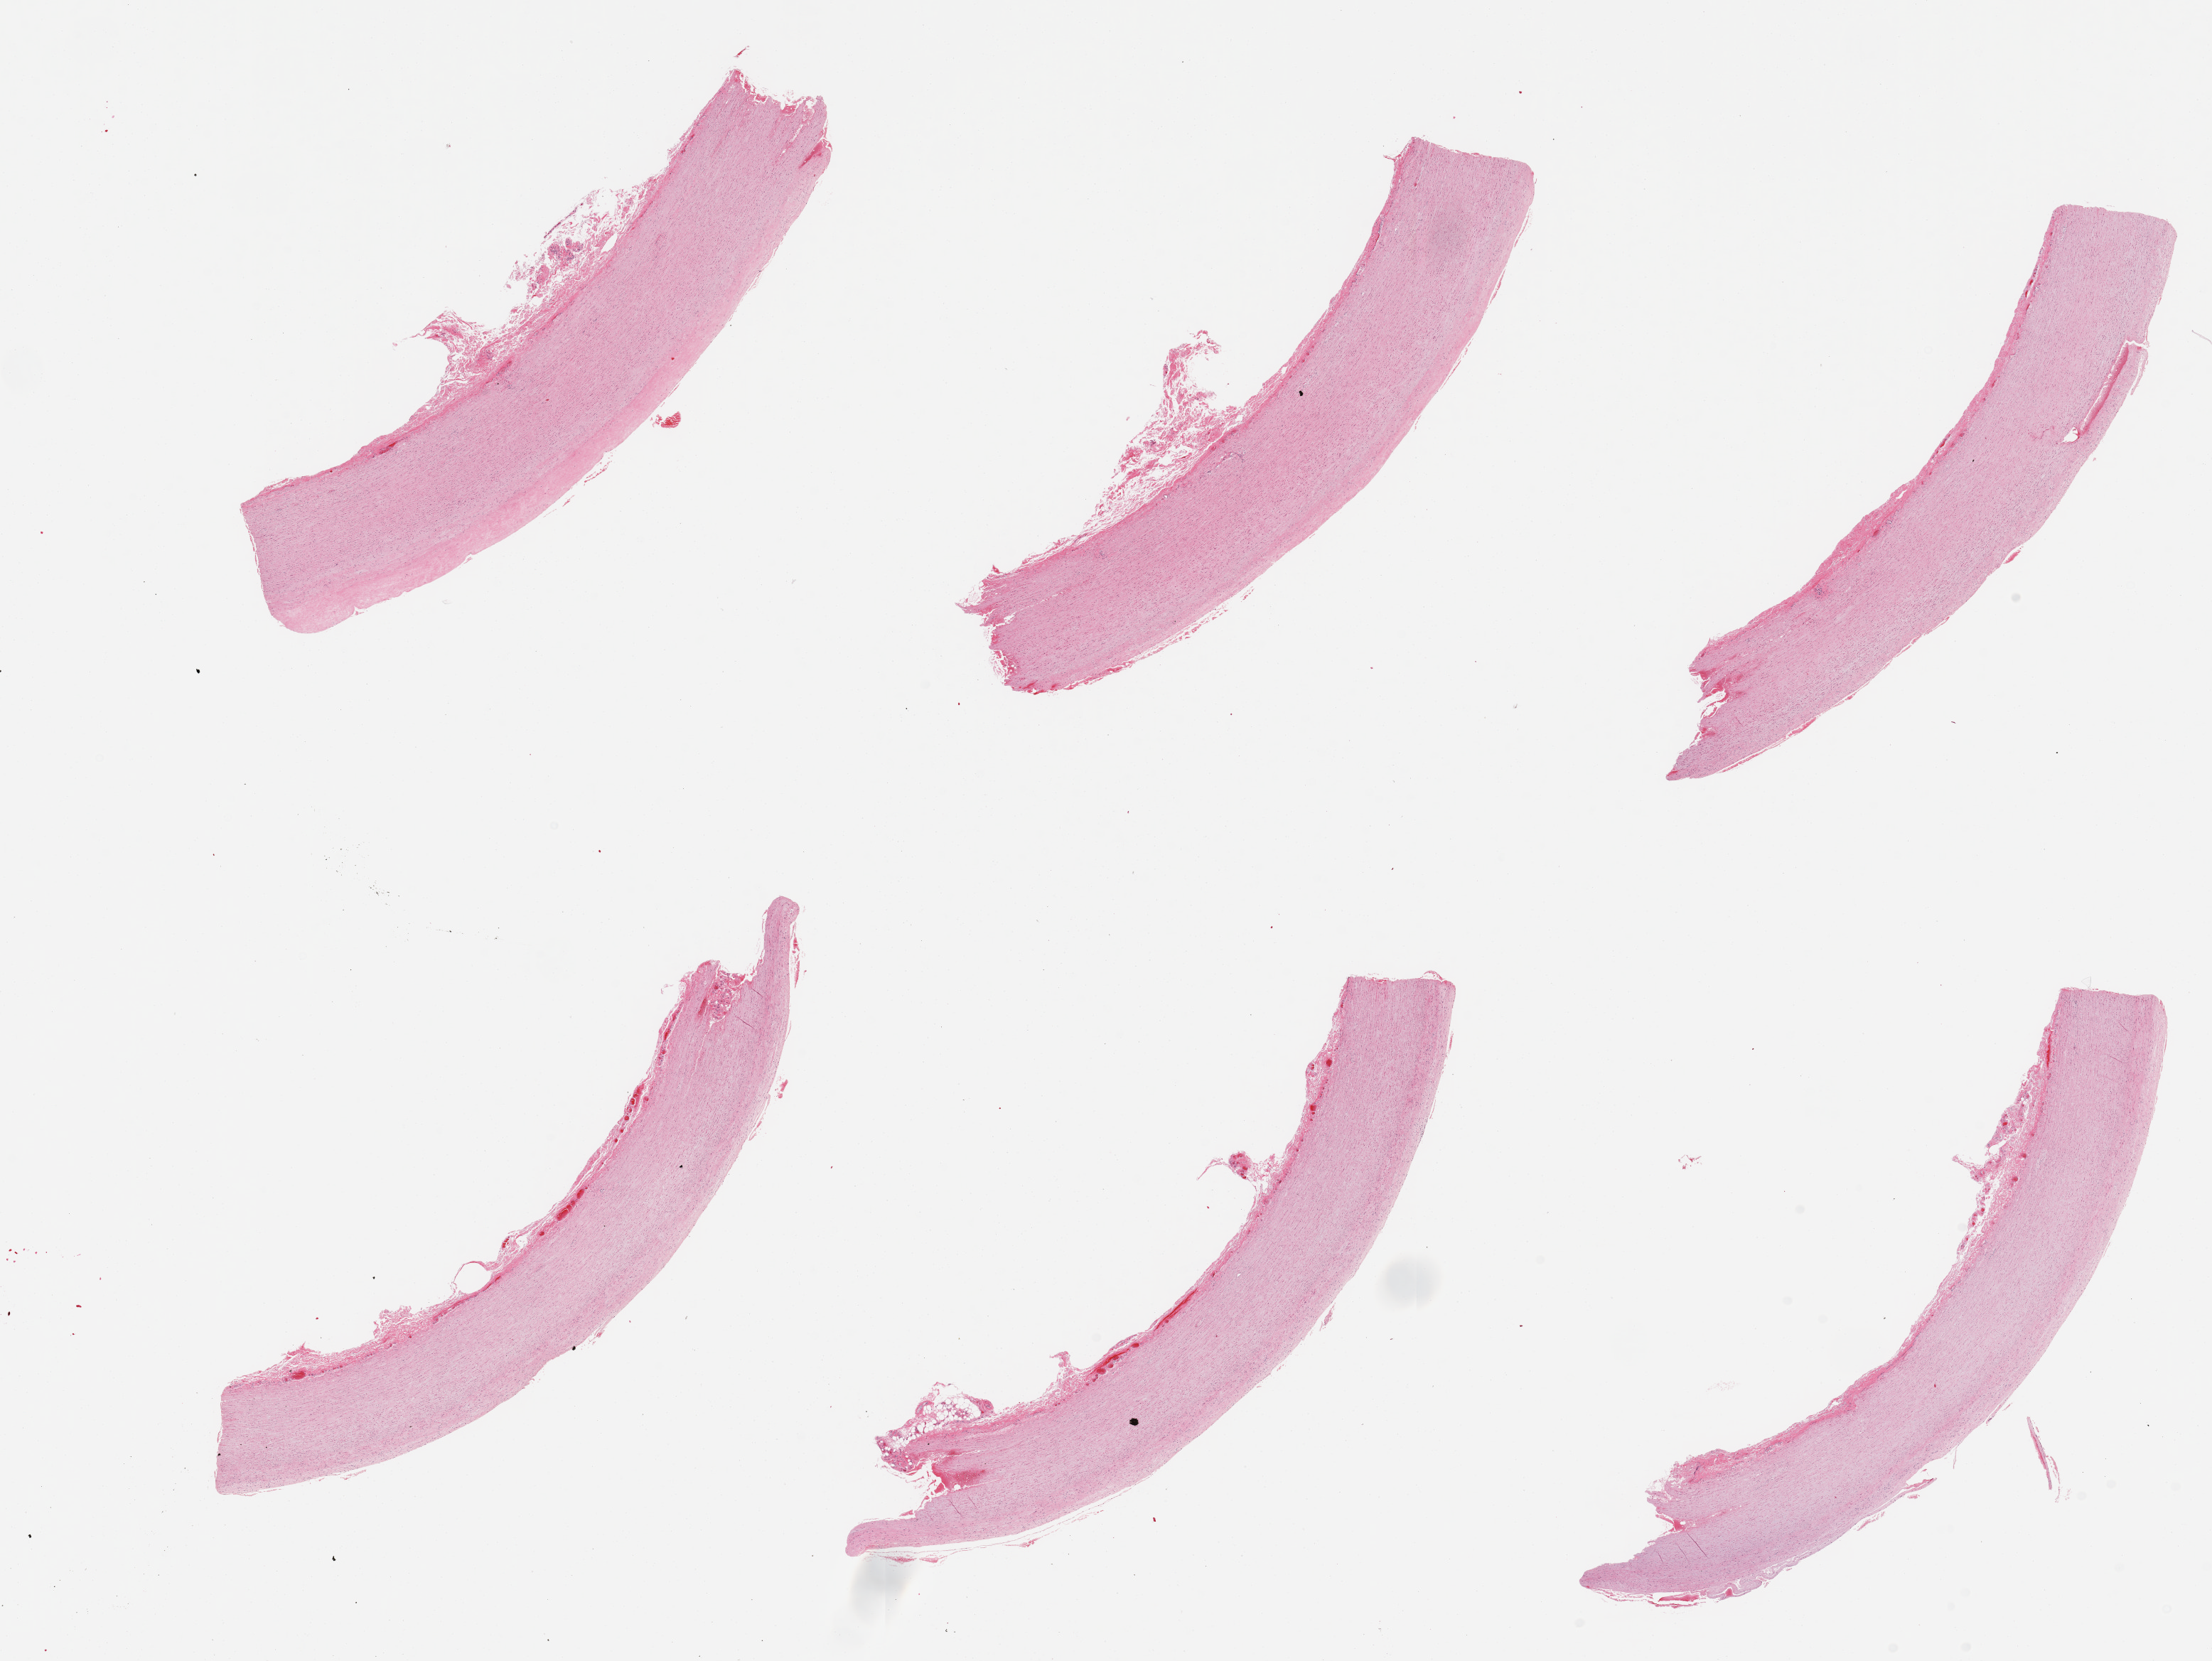
Whole-slide image, hematoxylin and eosin (H&E) stain — low-resolution overview of the scanned area, about 24.6 x 18.5 mm (acquisition: 20x scan). PAXgene-fixed, paraffin-embedded tissue. Section of aorta (target tissue). Tissue donor sample.
Pathologist's review note for this sample: 6 pieces; fiber (elastic?) drop out; minimal plaque.